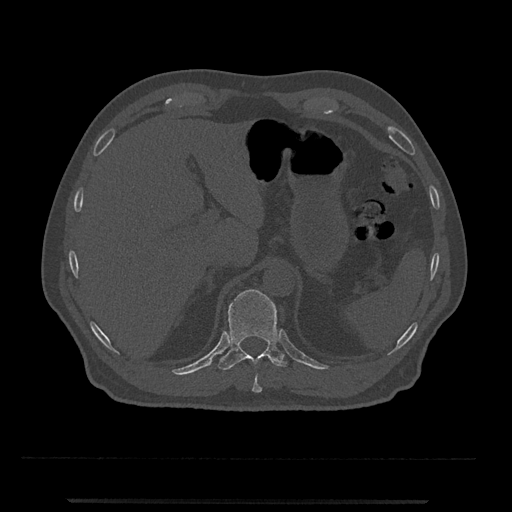
CT including the spine, one axial slice; slice 476 of 797 in the series (ordered by position); reconstruction kernel Br40s/3; 120 kVp; bone window (W 1800 / L 400 HU); 0.5 mm slice thickness; 512 × 512 image matrix, field of view 419 × 419 mm. Male patient, age 63 years. Case-level facts recorded for this patient, not image findings: primary cancer: prostate.
Annotated regions visible in this slice (semi-automatically segmented with operator editing):
- T10 vertebra: bounding box <252,375,262,393> (left, top, right, bottom; pixels)
- T11 vertebra: <218,289,288,370>